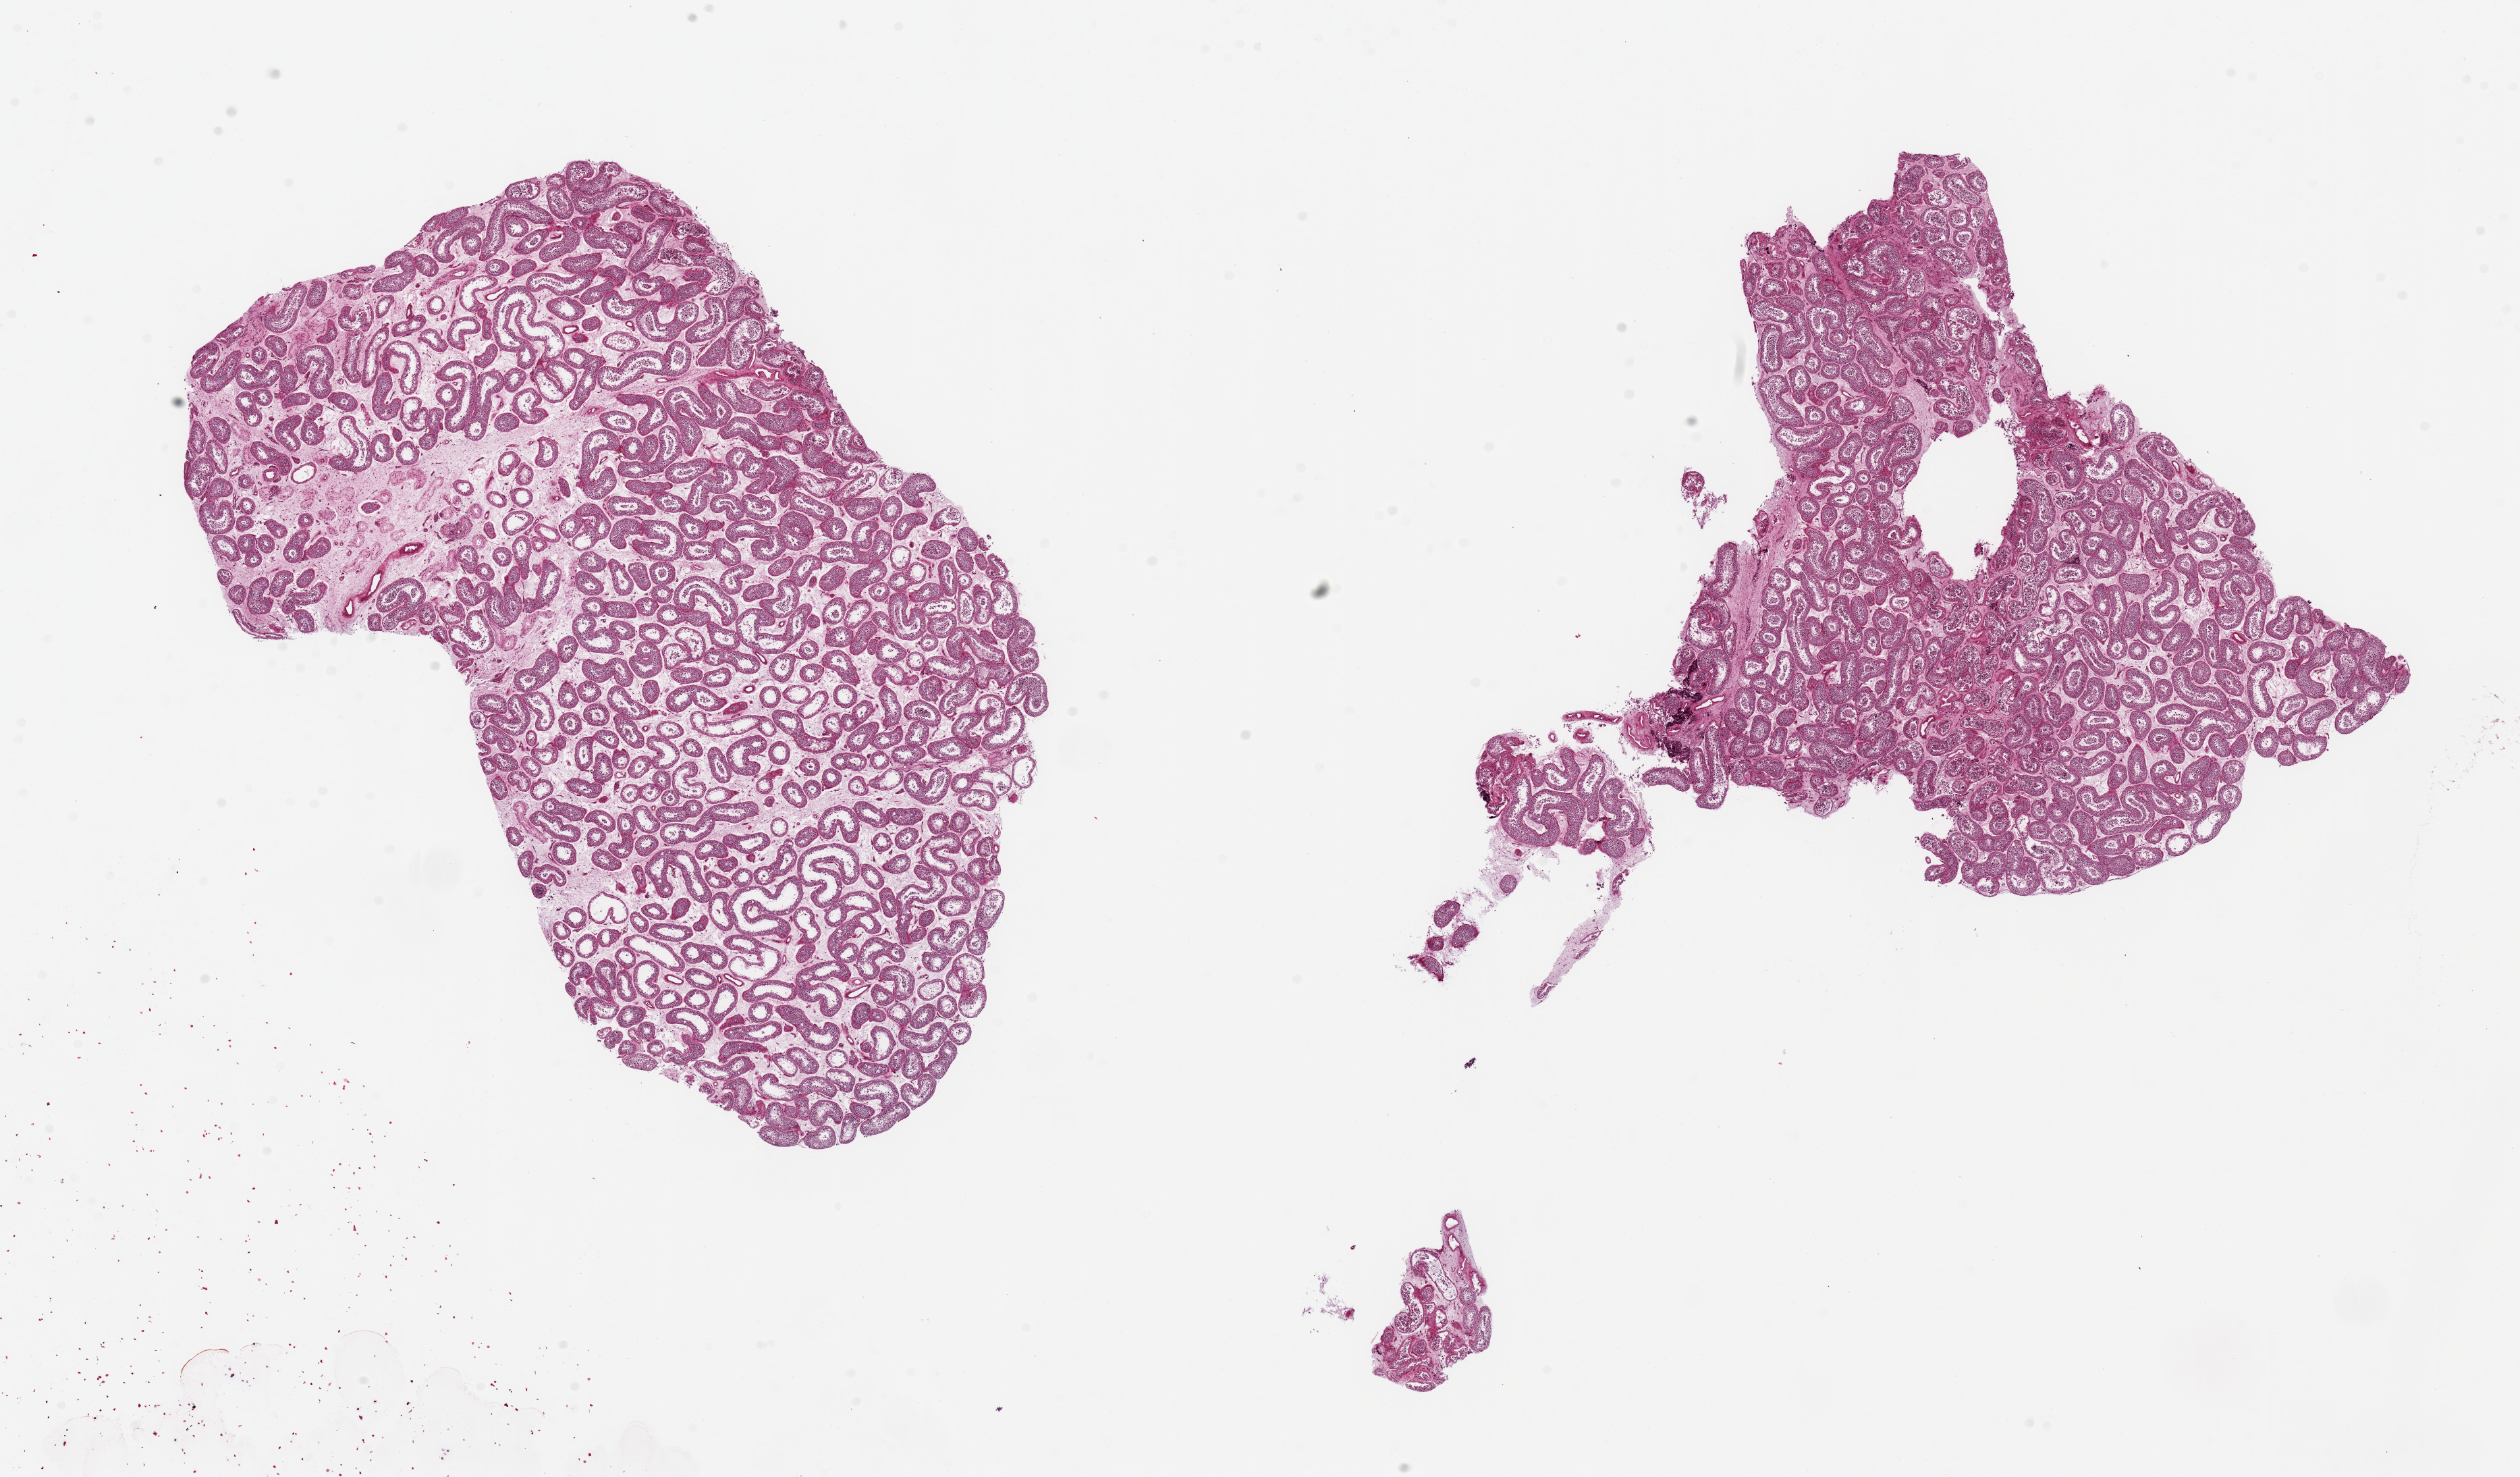
Digitized hematoxylin and eosin (H&E)-stained section, brightfield — low-resolution overview of the scanned area, about 29.5 x 17.3 mm. PAXgene-fixed paraffin-embedded (PFPE) section. Sampled site (target tissue): testis. Donor tissue sample.
Reviewer comment on this tissue sample: 2 pieces, 12x8 & 15x9mm; Larger piece shows reduced spermatogenesis.